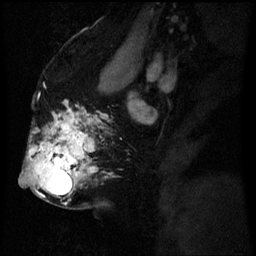
Breast MRI (dynamic contrast-enhanced), one sagittal slice. Slice 36 of 60 in the series (ordered by position). Dynamic contrast-enhanced series, image 2 of 3 at this slice position (ordered by acquisition). 1.5 T. TE 4.2 ms, TR 8 ms. 2.5 mm slice thickness. 256 × 256 image matrix, field of view 200 × 200 mm. Female patient, age 50 years.
Outlined on this slice (semi-automatic segmentation, software-assisted and operator-edited):
- analysis volume of interest (the breast-tissue region the enhancement analysis was run in; not a lesion): bounding box <24,114,93,203> (left, top, right, bottom; pixels)
- tumour enhancement mask (voxels above the 70 % enhancement threshold inside the analysis volume of interest): <30,120,93,195>